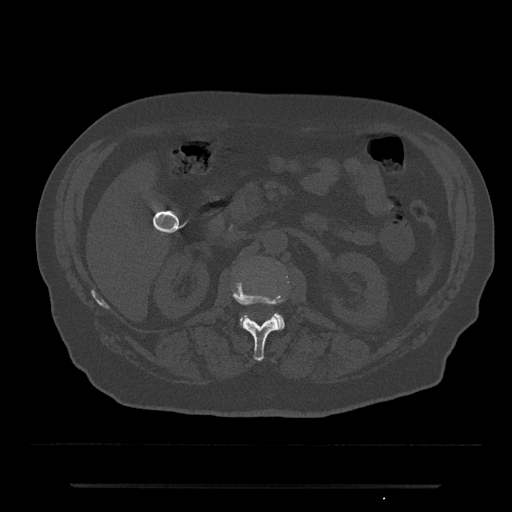
CT including the spine, one axial slice; slice 515 of 797 in the series (ordered by position); reconstruction kernel Br40s/3; bone window (W 1800 / L 400 HU); 0.5 mm slice thickness; 512 × 512 image matrix, field of view 434 × 434 mm. Male patient, age 80 years. Case-level facts recorded for this patient, not image findings: primary cancer: prostate.
Annotated regions visible in this slice (semi-automatic segmentation, software-assisted and operator-edited):
- L1 vertebra: box from (x=233, y=282) to (x=284, y=361) px
- L2 vertebra: (x=239, y=313)–(x=285, y=331)